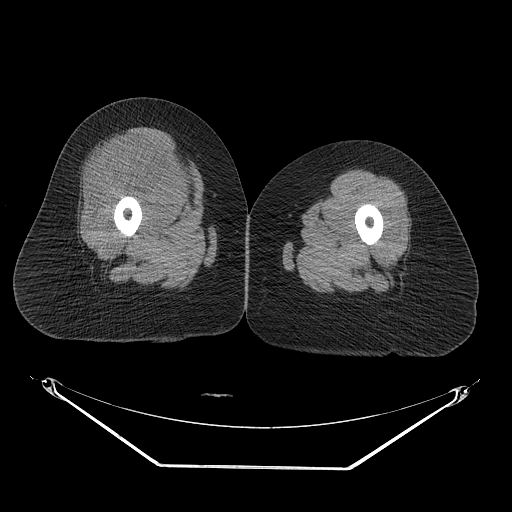
CT of an extremity soft-tissue mass (from a PET/CT study), one axial slice. Position 30 of 267 along the scan axis. Reconstruction kernel STANDARD. Soft-tissue window (W 400 / L 40 HU). 512 × 512 image matrix, field of view 500 × 500 mm. Female patient. From the clinical record (not read from this slice): histological type: malignant solitary fibrous tumor; grade: intermediate; site of the primary tumour: right thigh.
Structures marked on this image (expert contour drawn on MRI and transferred to this co-registered scan by the dataset authors):
- gross tumour volume including surrounding oedema: bounding box <96,132,204,218> (left, top, right, bottom; pixels)
- gross tumour volume (mass): <100,132,200,213>